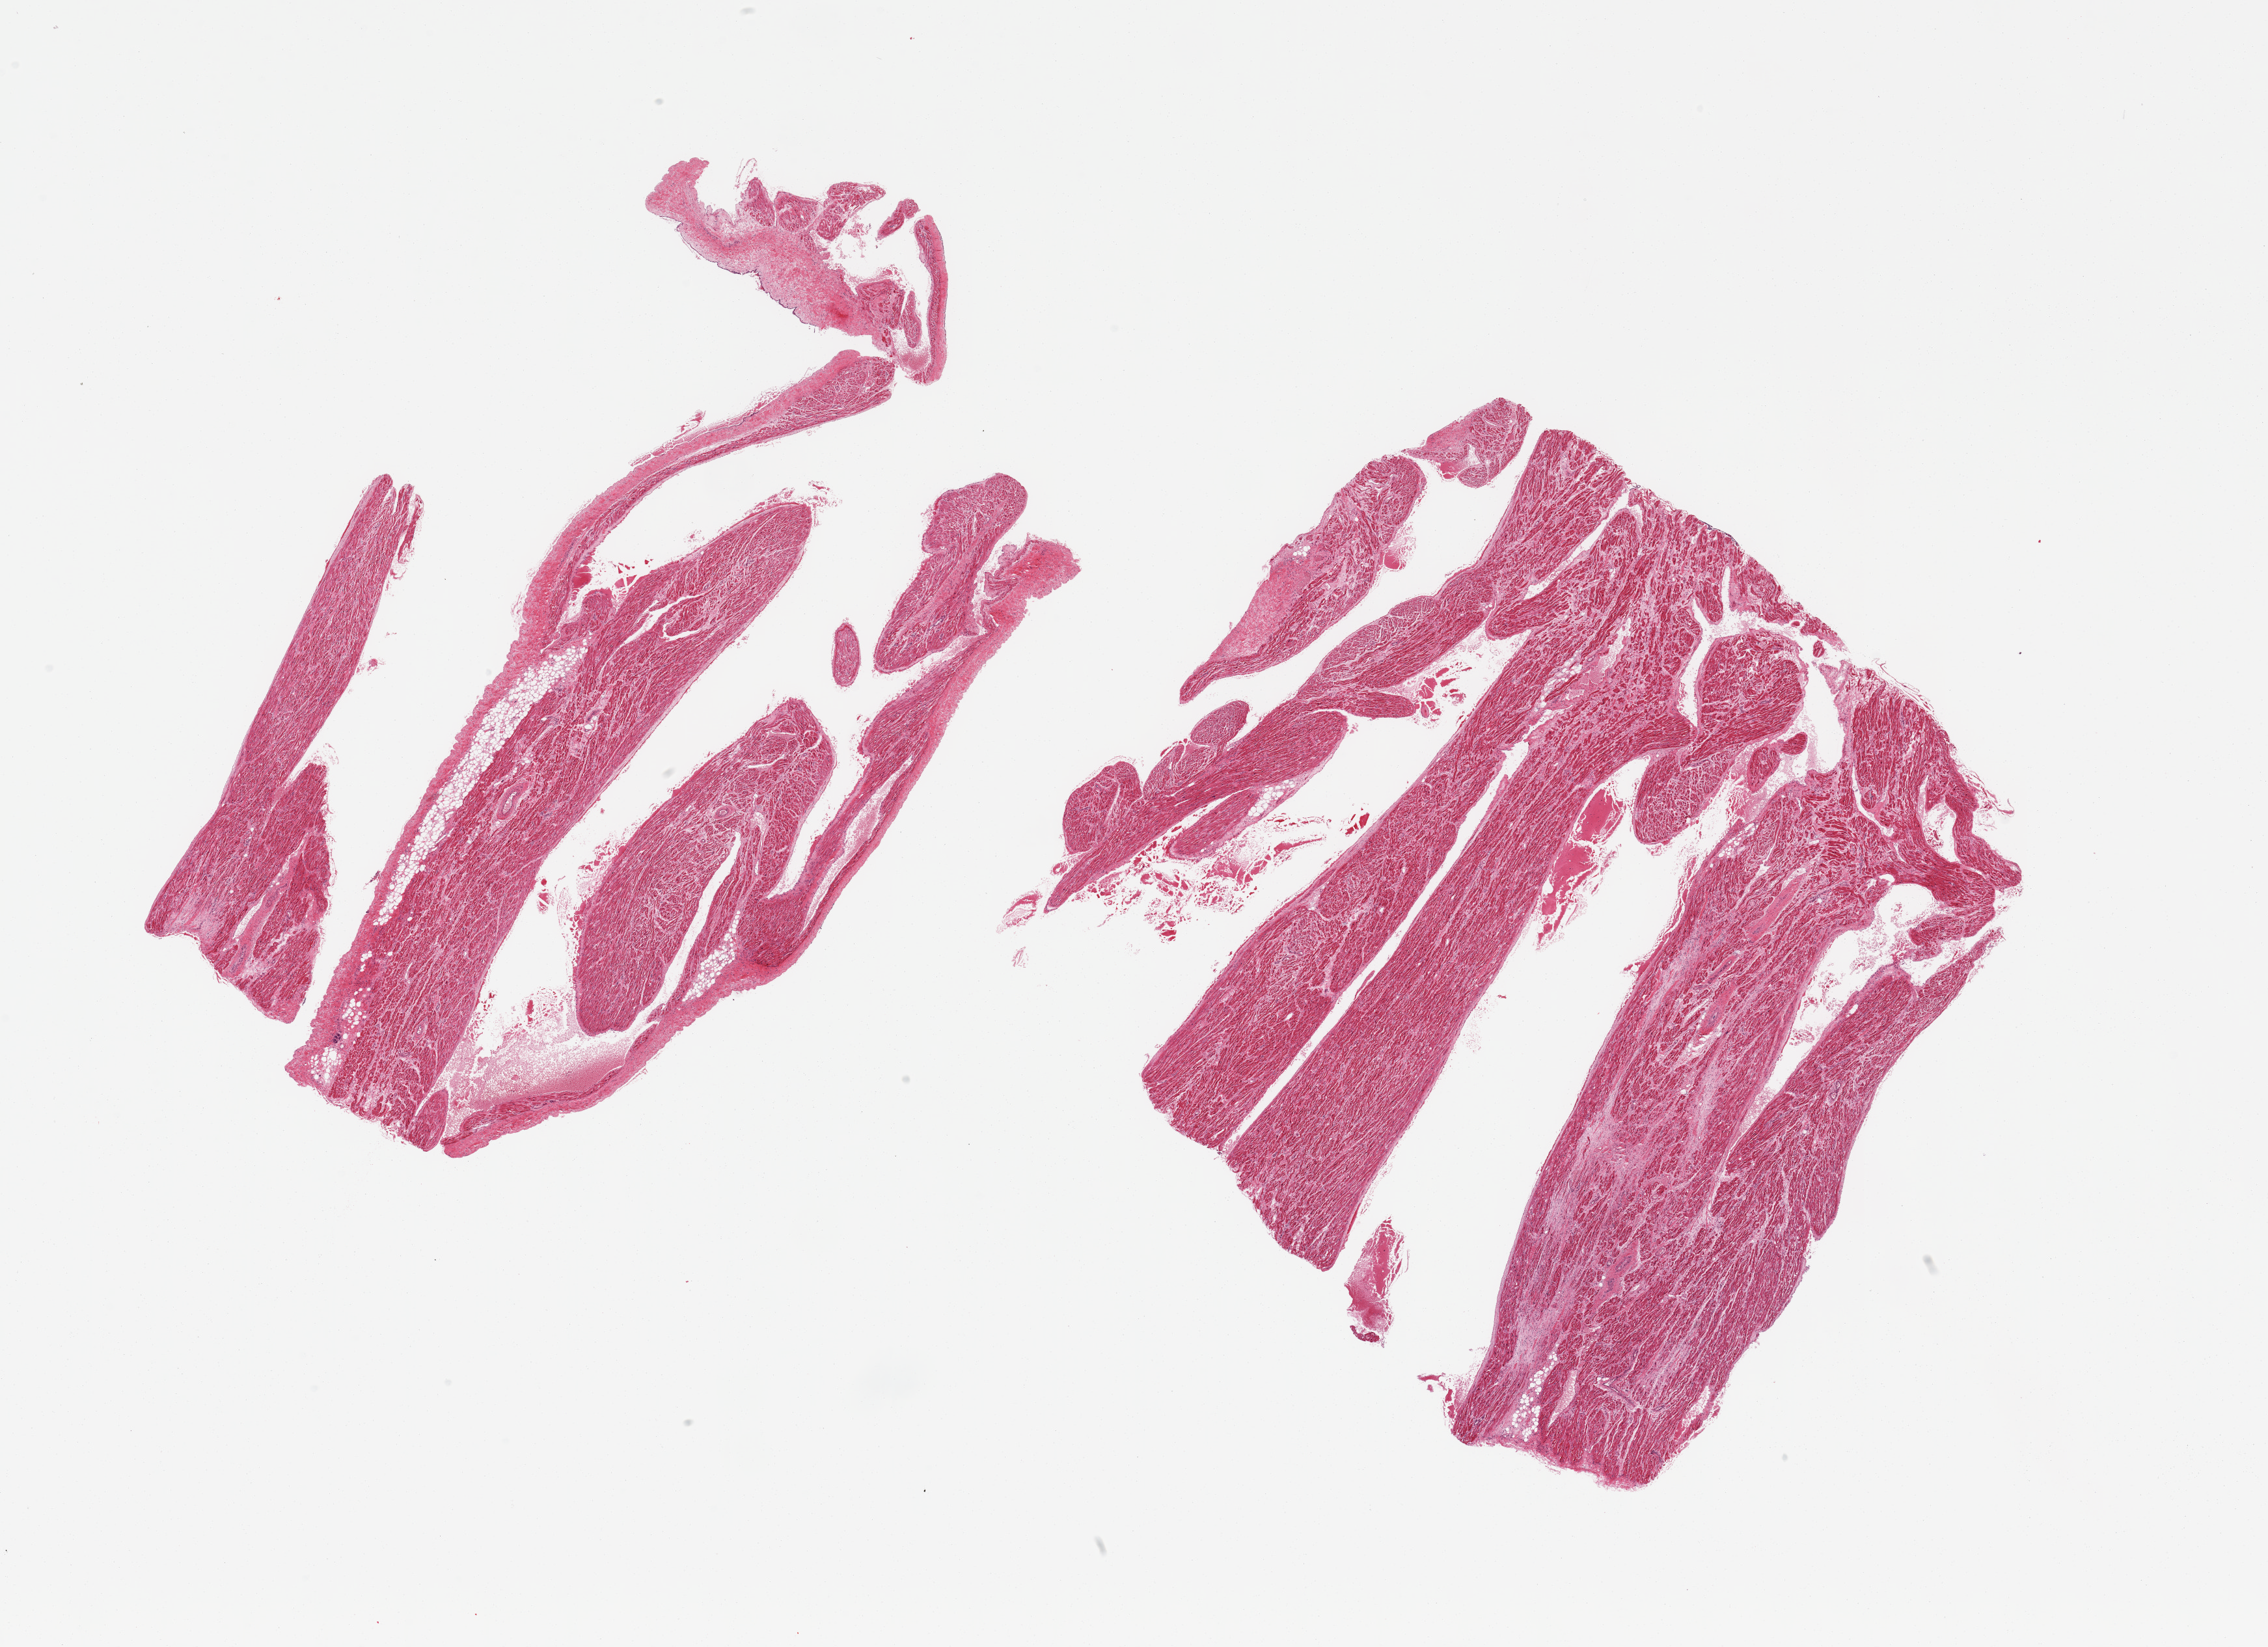
Whole-slide image, hematoxylin and eosin (H&E) stain, brightfield — shown as a low-resolution overview of the whole scanned area (about 27.6 x 20.0 mm, from a 20x scan); PAXgene-fixed paraffin-embedded (PFPE) section; sampled site (target tissue): auricular appendage; donor tissue sample. Donor: male.
• pathologist's review note for this sample: 2 pieces; 10% internal fat